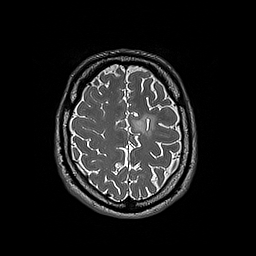
Brain MRI from a brain-tumour surgery series, one axial slice. Position 56 of 192 along the scan axis. 1 mm slice thickness. 256 × 256 image matrix, field of view 250 × 250 mm. Case-level facts recorded for this patient, not image findings: histopathology: Oligodendroglioma; WHO grade: 3; IDH mutation: yes.
Structures marked on this image (expert manual segmentation):
- tumour: bounding box (x1, y1, x2, y2) in pixels: (132, 114, 157, 136)